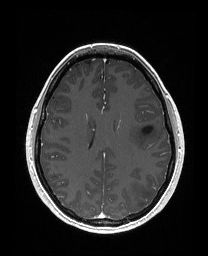
Brain MRI from a brain-tumour surgery series, one axial slice. Slice 103 of 176 in the series (ordered by position). T1-weighted post-contrast. 1 mm slice thickness. 208 × 256 image matrix, field of view 203 × 250 mm. From the clinical record (not read from this slice): histopathology: Astrocytoma; WHO grade: 3; IDH mutation: yes; tumour location: Left Frontal.
Structures marked on this image (outlined manually by an expert reader):
- tumour: bounding box (x1, y1, x2, y2) in pixels: (128, 121, 159, 148)